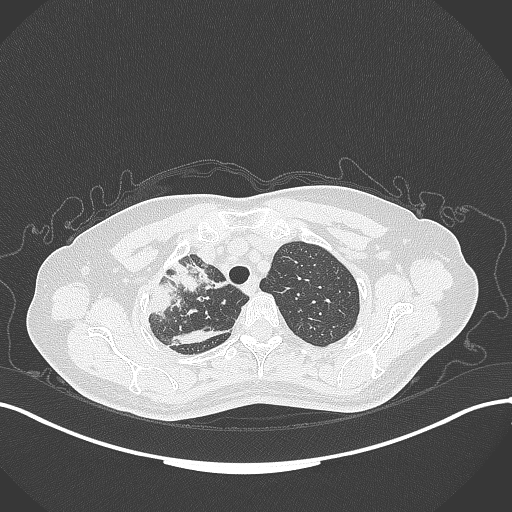
Chest CT, one axial slice; position 264 of 309 along the scan axis; reconstruction kernel B70f; 120 kVp; lung window (W 1500 / L -600 HU); 512 × 512 image matrix. Patient: female, 60 years. From the clinical record (not read from this slice): clinical TNM (as recorded): T3 N1 M1.
Structures marked on this image (rectangle marked by the reading radiologist):
- lung tumour (recorded histology: adenocarcinoma): bounding box [x1, y1, x2, y2] px = [144, 257, 226, 317]